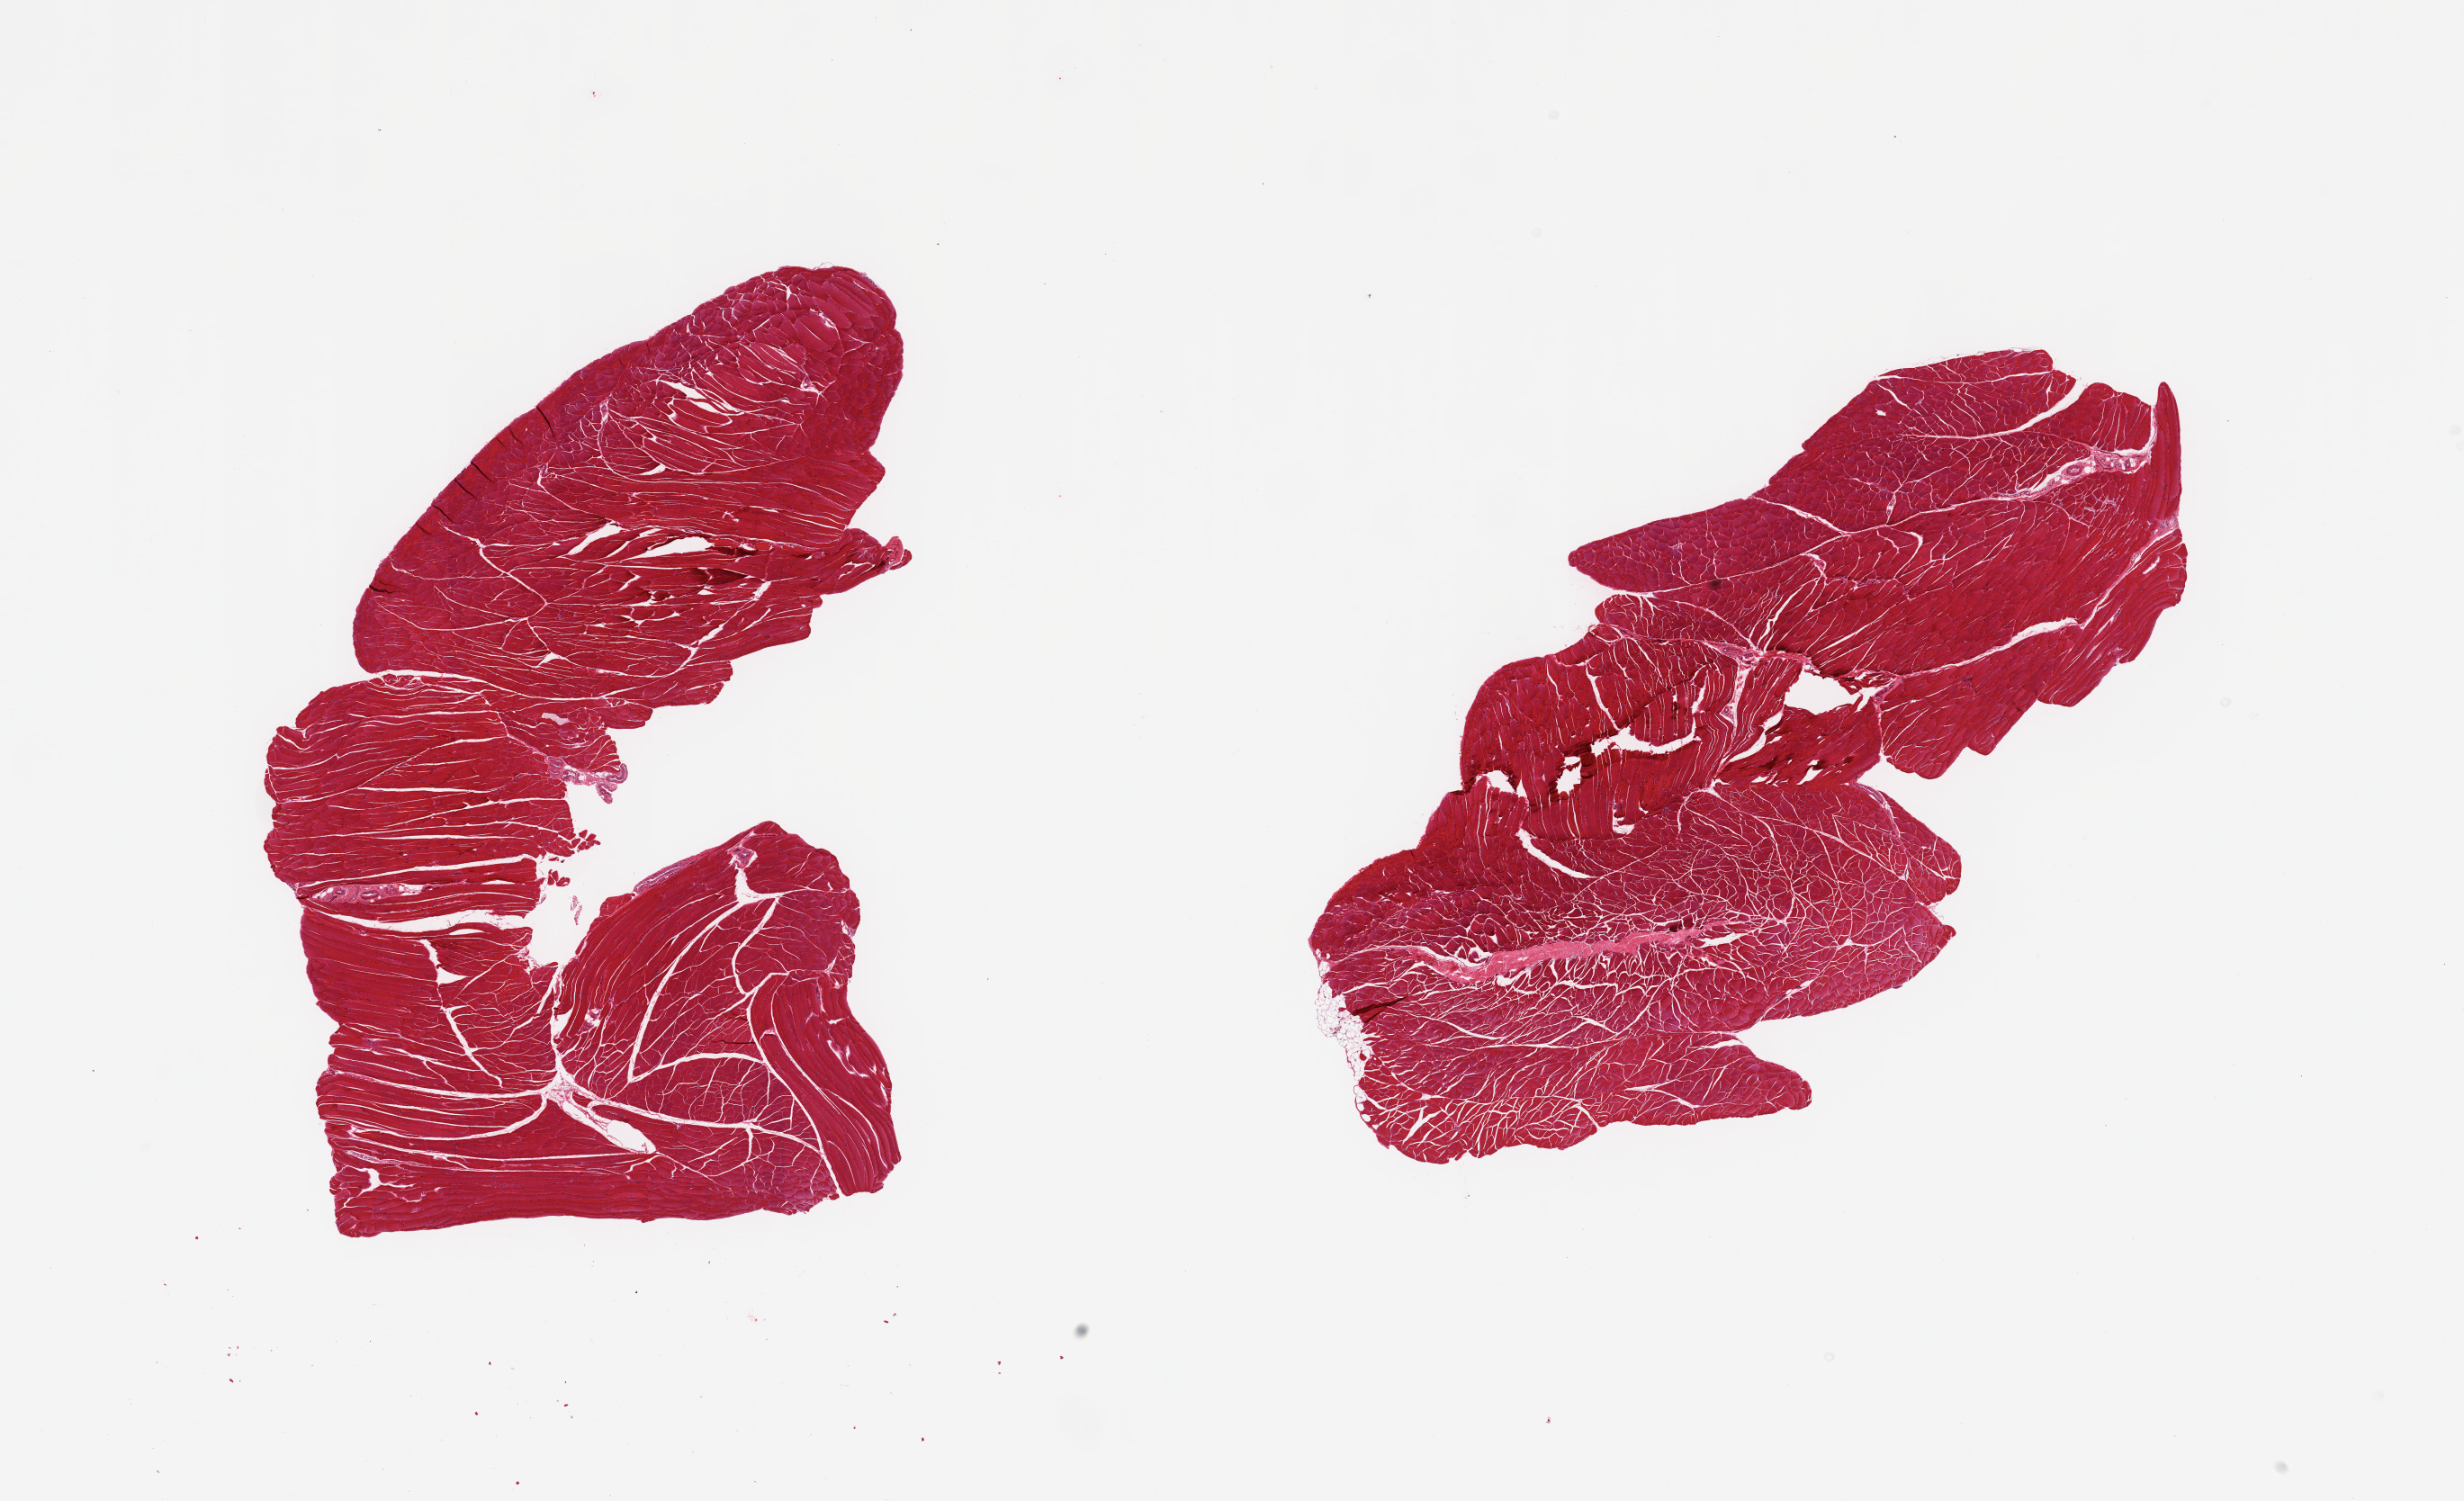
Digitized hematoxylin and eosin (H&E)-stained section, low-resolution overview of the scanned area, about 21.7 x 13.2 mm (from a 20x scan). PAXgene-fixed, paraffin-embedded tissue. Target tissue: skeletal muscle. Tissue donor sample.
Reviewer comment on this tissue sample: 2 pieces, minimal interstitial fat.